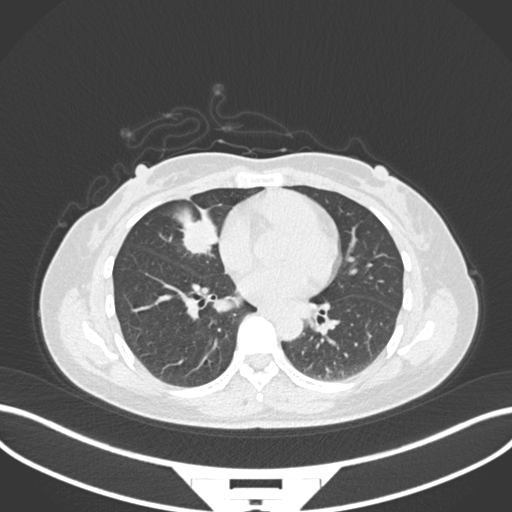
Chest CT, one axial slice. Position 74 of 171 along the scan axis. Reconstruction kernel B30f. 120 kVp. Lung window (W 1500 / L -600 HU). 1 mm slice thickness. 512 × 512 image matrix, field of view 400 × 400 mm. Female patient, age 43 years. From the clinical record (not read from this slice): clinical TNM (as recorded): T1c N3 M1; histopathological grade: G1.
Outlined on this slice (rectangle marked by the reading radiologist):
- lung tumour (recorded histology: adenocarcinoma): bounding box [x1, y1, x2, y2] px = [174, 209, 219, 257]